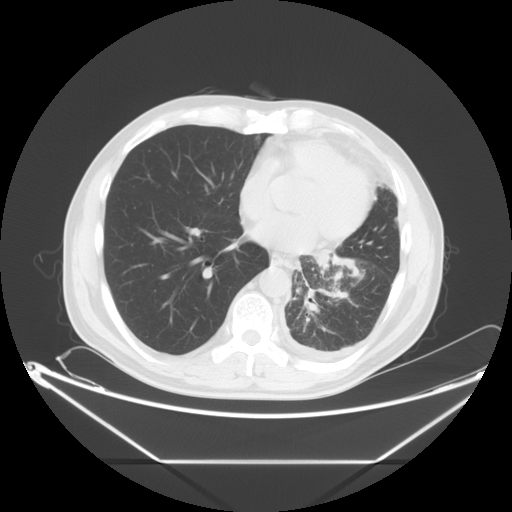
Chest CT, one axial slice; slice 26 of 63 in the series (ordered by position); 120 kVp; lung window (W 1500 / L -600 HU); 5 mm slice thickness; 512 × 512 image matrix. Male patient, age 60 years. From the clinical record (not read from this slice): clinical TNM (as recorded): T4 N1 M1.
Outlined on this slice (rectangle marked by the reading radiologist):
- lung tumour (recorded histology: adenocarcinoma): bounding box <312,244,369,295> (left, top, right, bottom; pixels)